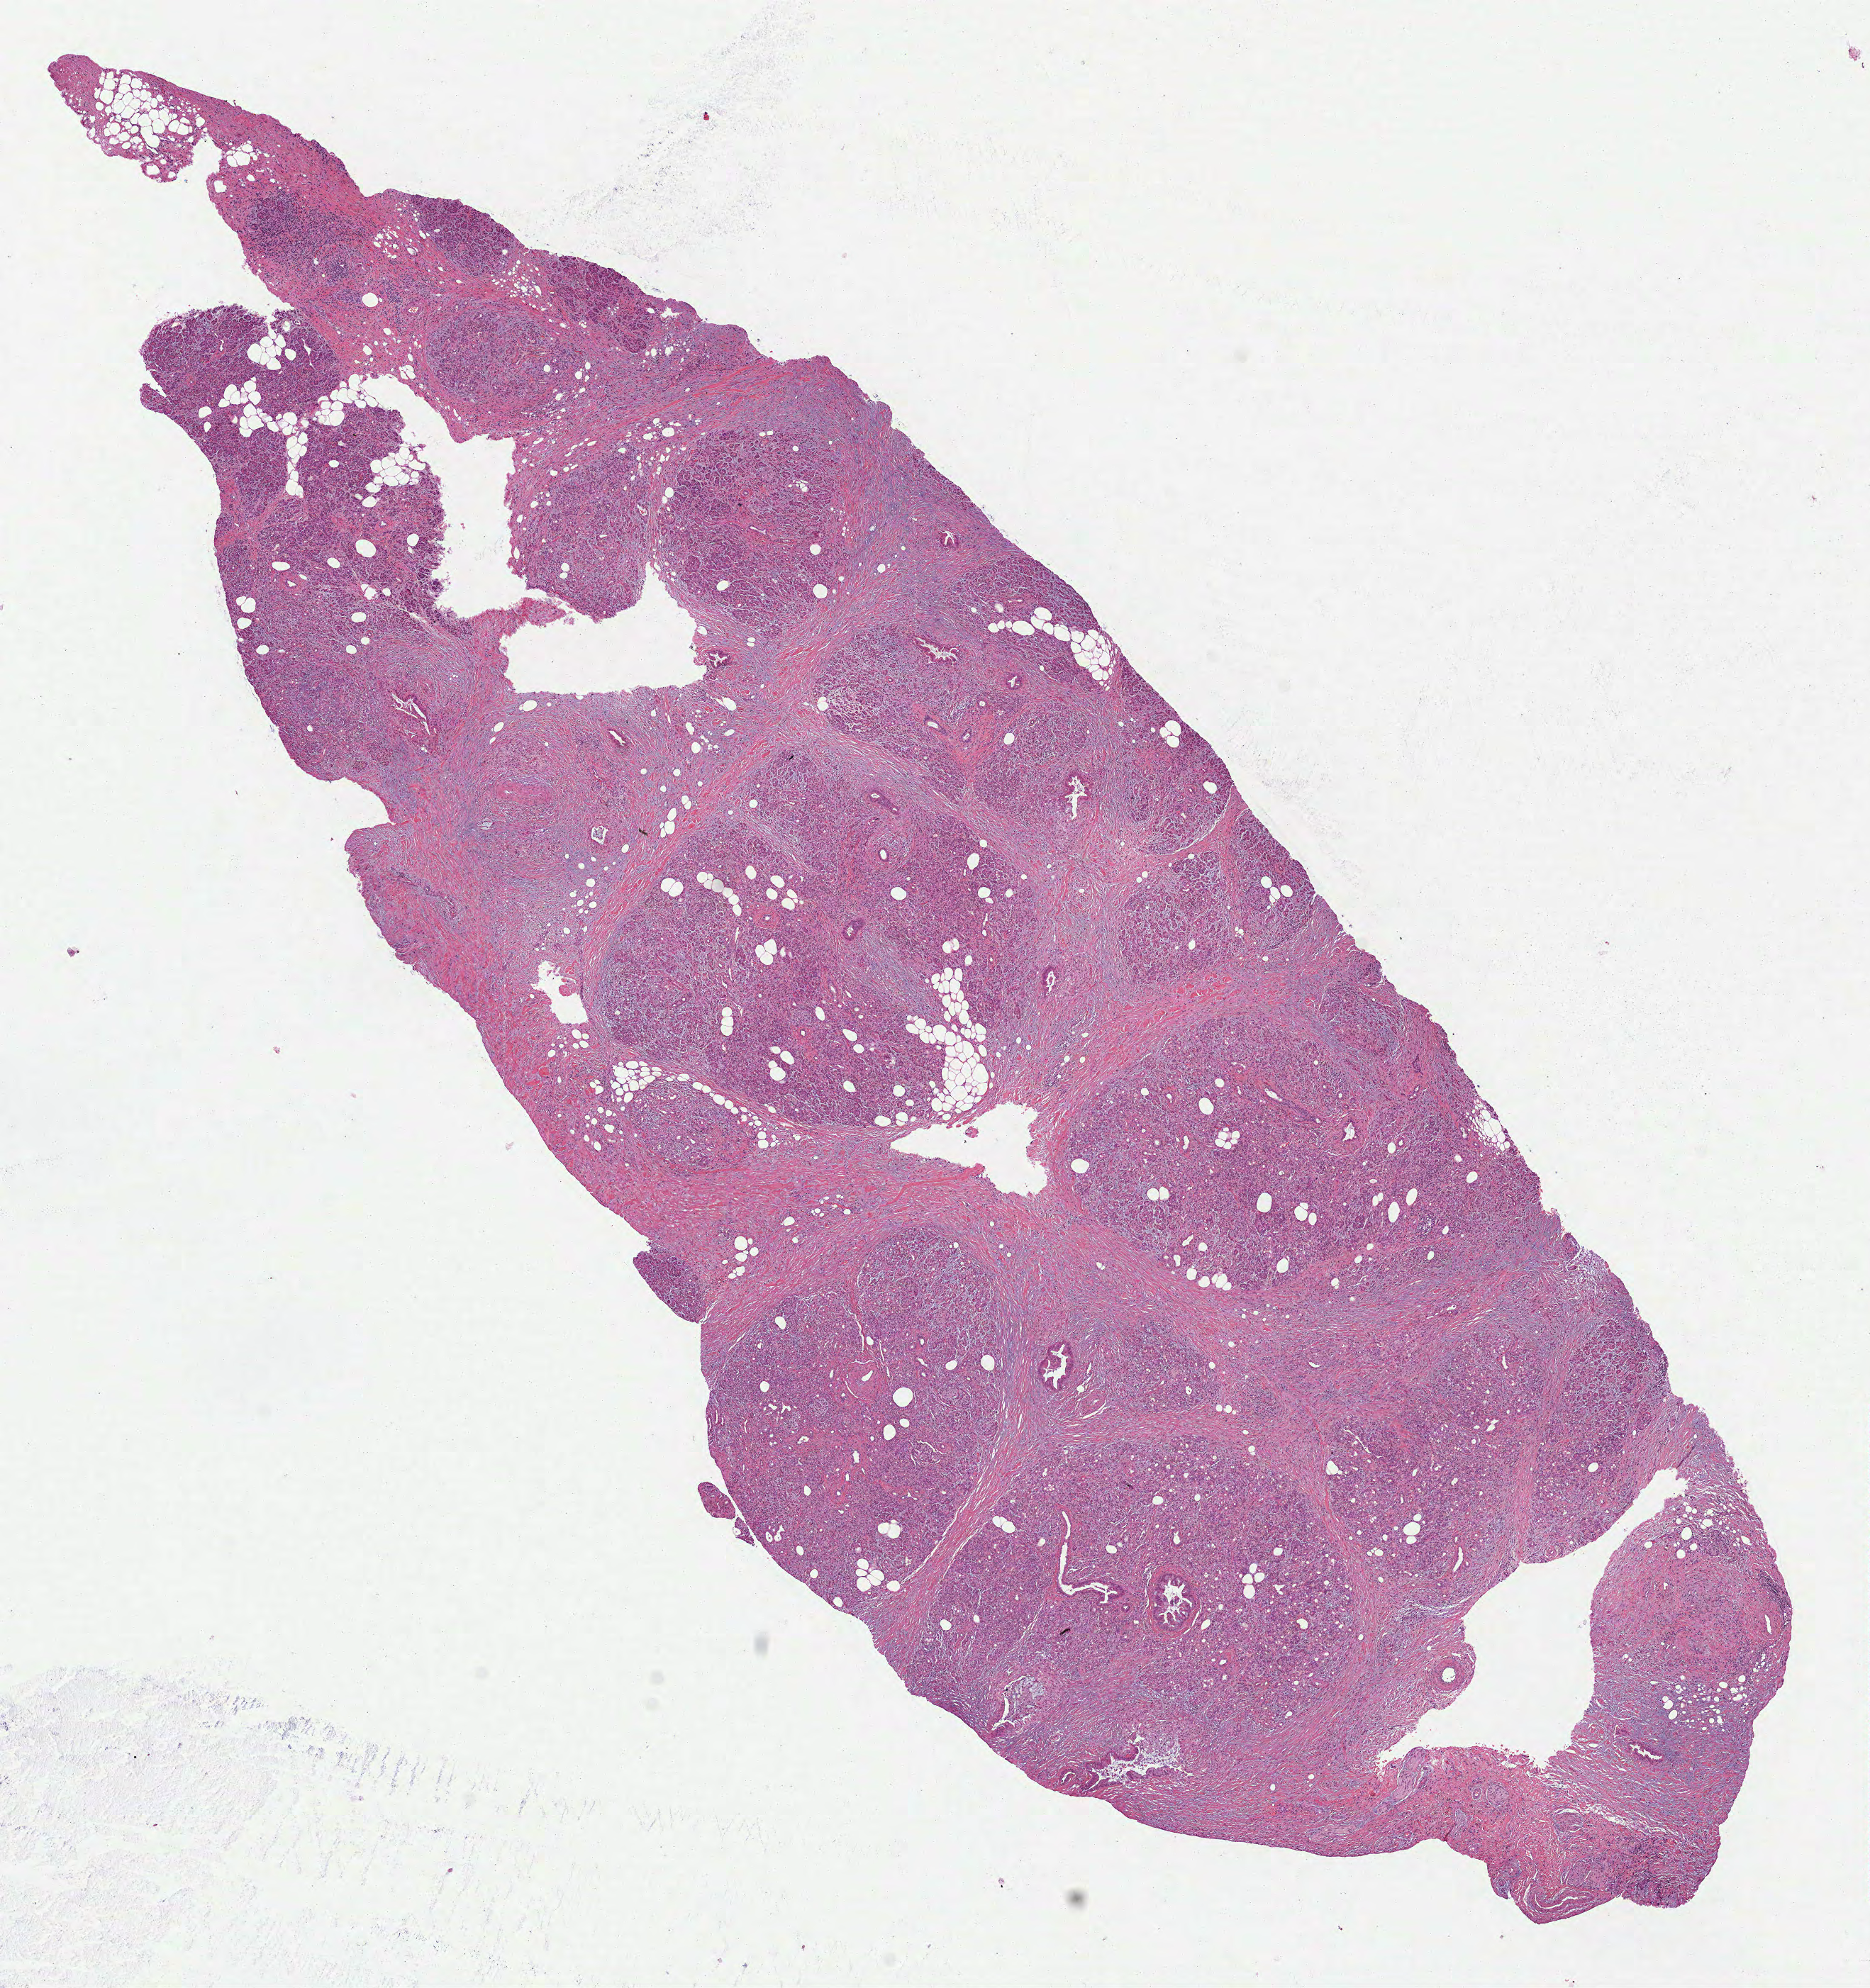
Digitized H&E-stained tissue section (whole slide), shown as a low-resolution overview of the whole scanned area (about 10.6 x 11.3 mm). Formalin-fixed paraffin-embedded (FFPE) diagnostic section. Sample: primary tumour, pancreas. Female patient; age at initial diagnosis 58 years. Histologic grade: G2 (moderately differentiated).
- AJCC pathologic stage: IIB (7th edition)
- pathologic diagnosis: Infiltrating duct carcinoma, NOS (head of pancreas)